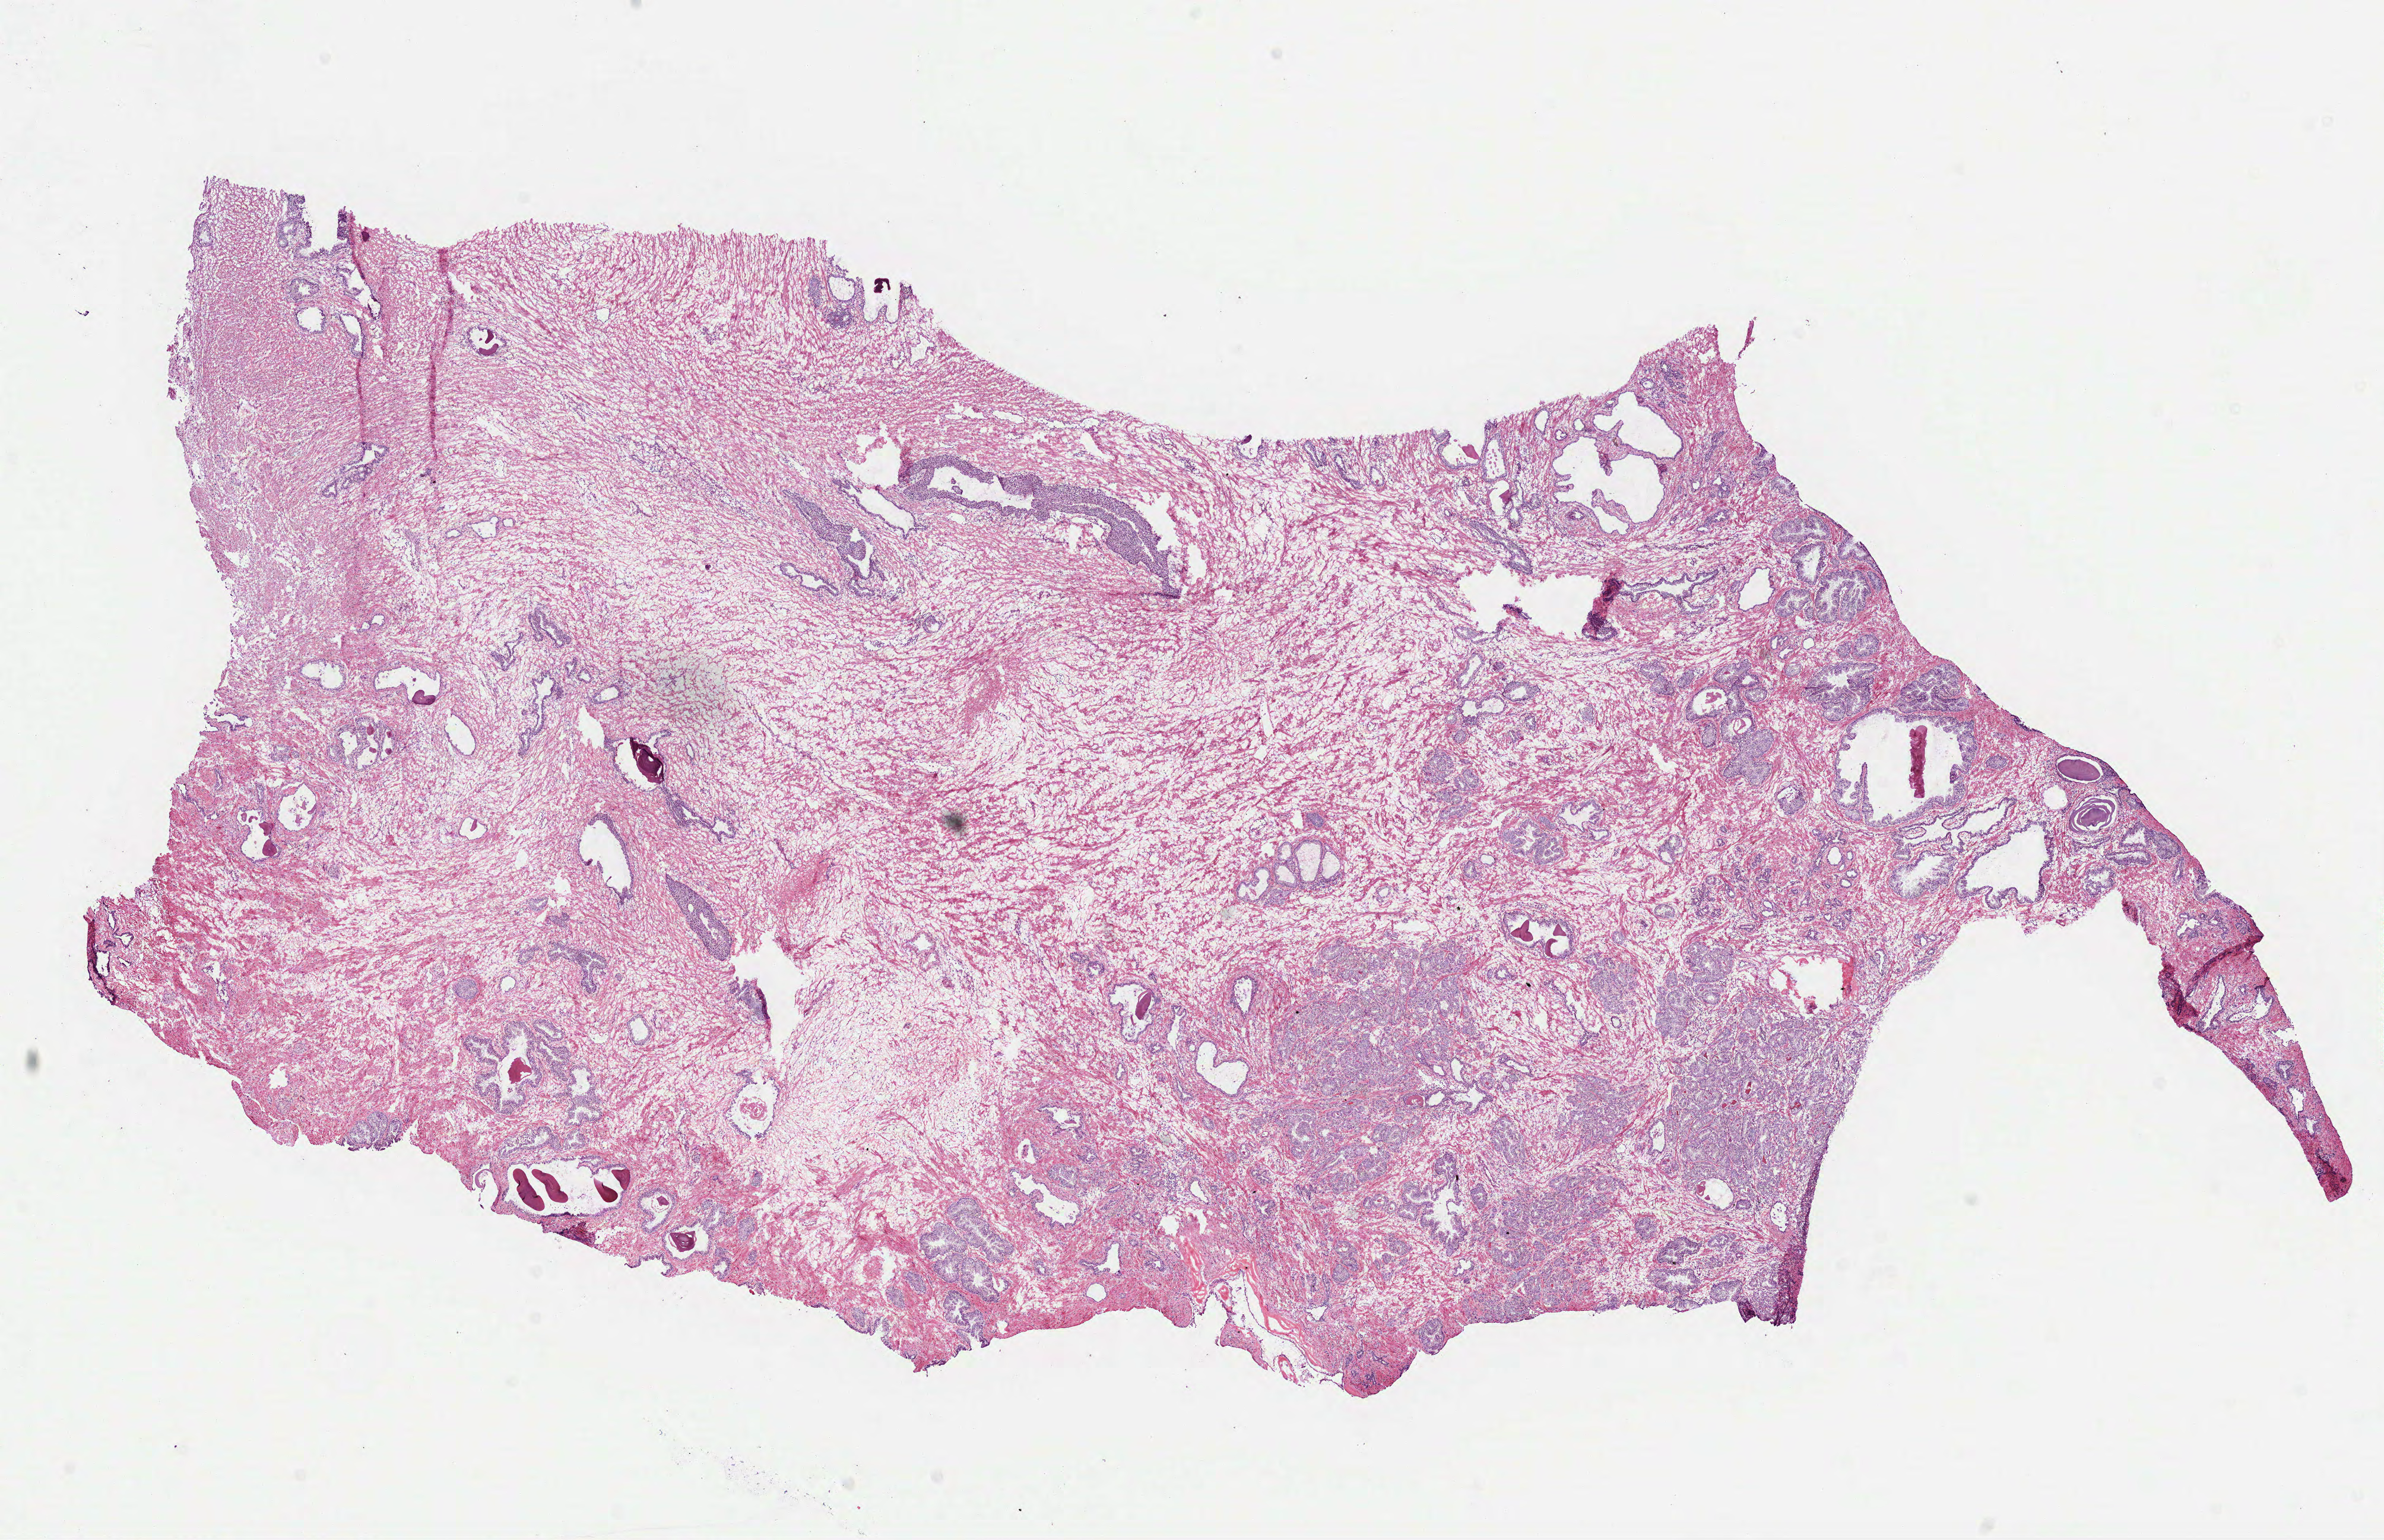
H&E whole-slide image, shown as a low-resolution overview of the whole scanned area (about 16.2 x 10.5 mm, acquisition: 40x scan); frozen section from the bottom of the tissue portion; primary tumour sample from the prostate. Patient: male, age at initial diagnosis 67 years. Gleason score: 7 (3+4). Pathologist review of this section (percent, as recorded): tumour cells 20%, tumour nuclei 40%, normal cells 30%, stromal cells 50%, necrosis 0%. Inflammatory infiltration, as recorded: lymphocyte infiltration 0%, monocyte infiltration 0%, neutrophil infiltration 0%.
• diagnosis: Acinar cell carcinoma (prostate gland)
• laterality: bilateral
• lymph nodes positive (case pathology): 0 of 11 examined